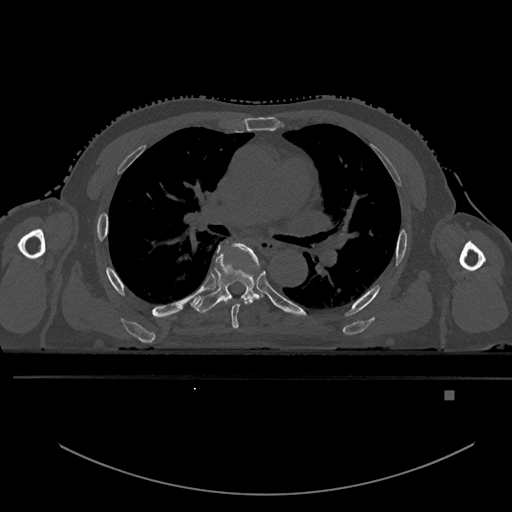
CT including the spine, one axial slice; bone window (W 1800 / L 400 HU); 0.5 mm slice thickness; 512 × 512 image matrix, field of view 456 × 456 mm. Patient: male, 82 years. Case-level facts recorded for this patient, not image findings: primary cancer: prostate.
Structures marked on this image (semi-automatically segmented with operator editing):
- T5 vertebra: bounding box <224,242,260,329> (left, top, right, bottom; pixels)
- T6 vertebra: <191,242,262,314>